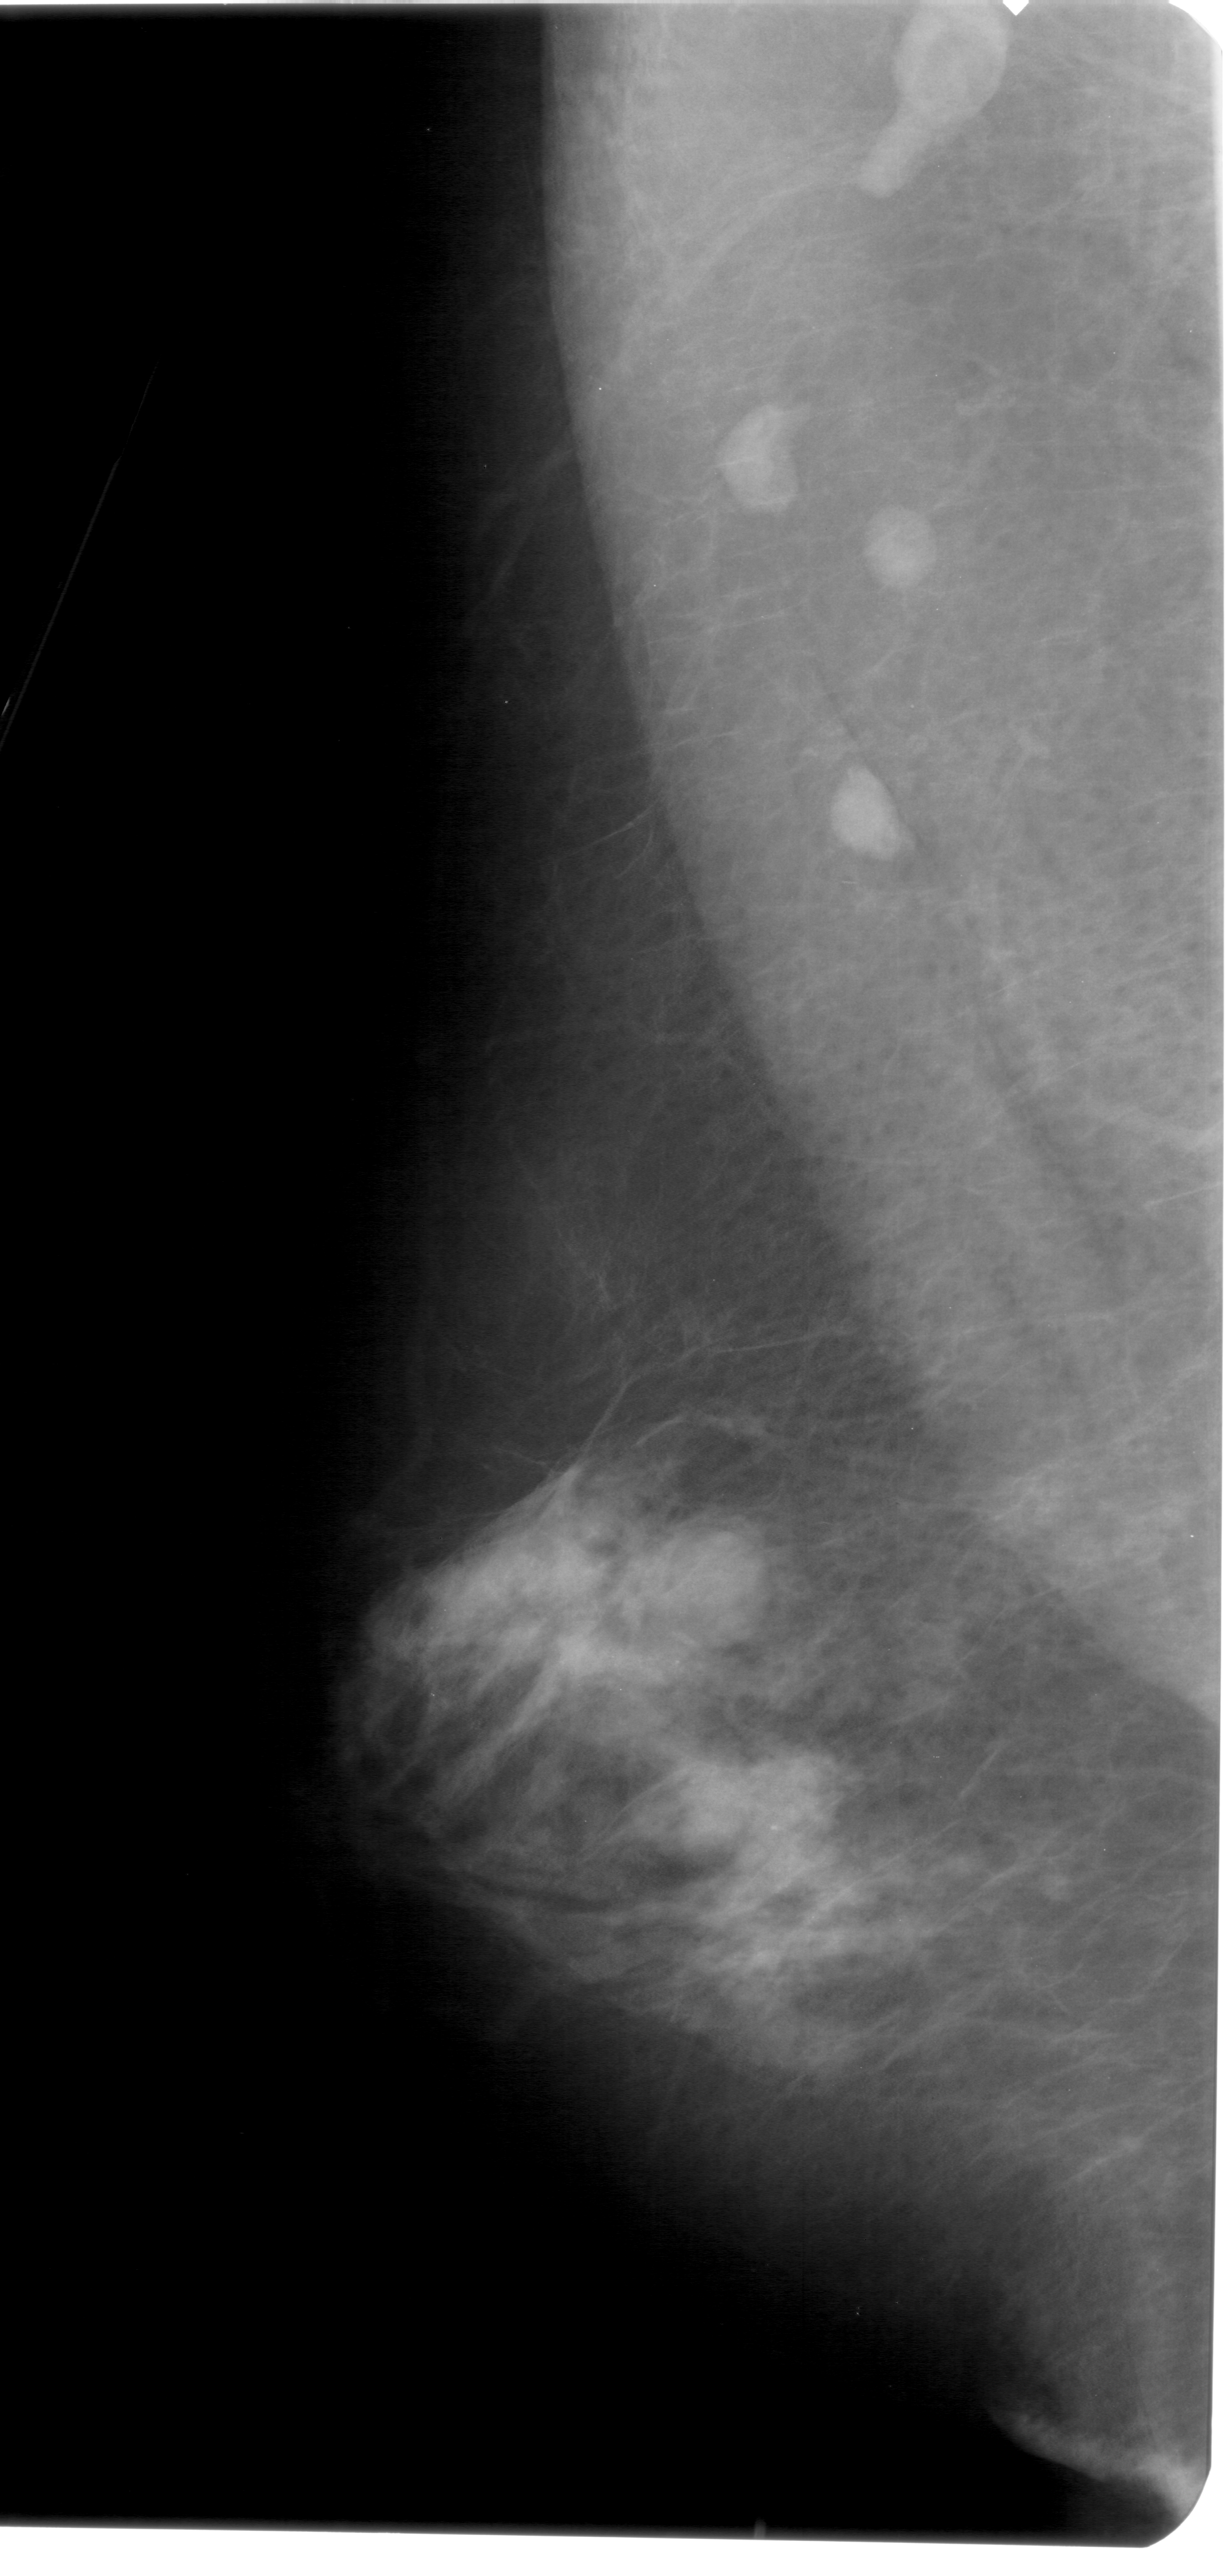
Digitized screen-film mammogram, left breast, MLO view, breast composition: extremely dense (BI-RADS density category 4 of 4).
- Radiologist-marked abnormalities on this image: mass, shape round, margins circumscribed; BI-RADS assessment category 4; subtlety rating 3 on a 1 (subtle) to 5 (obvious) scale; pathology (as recorded): benign.